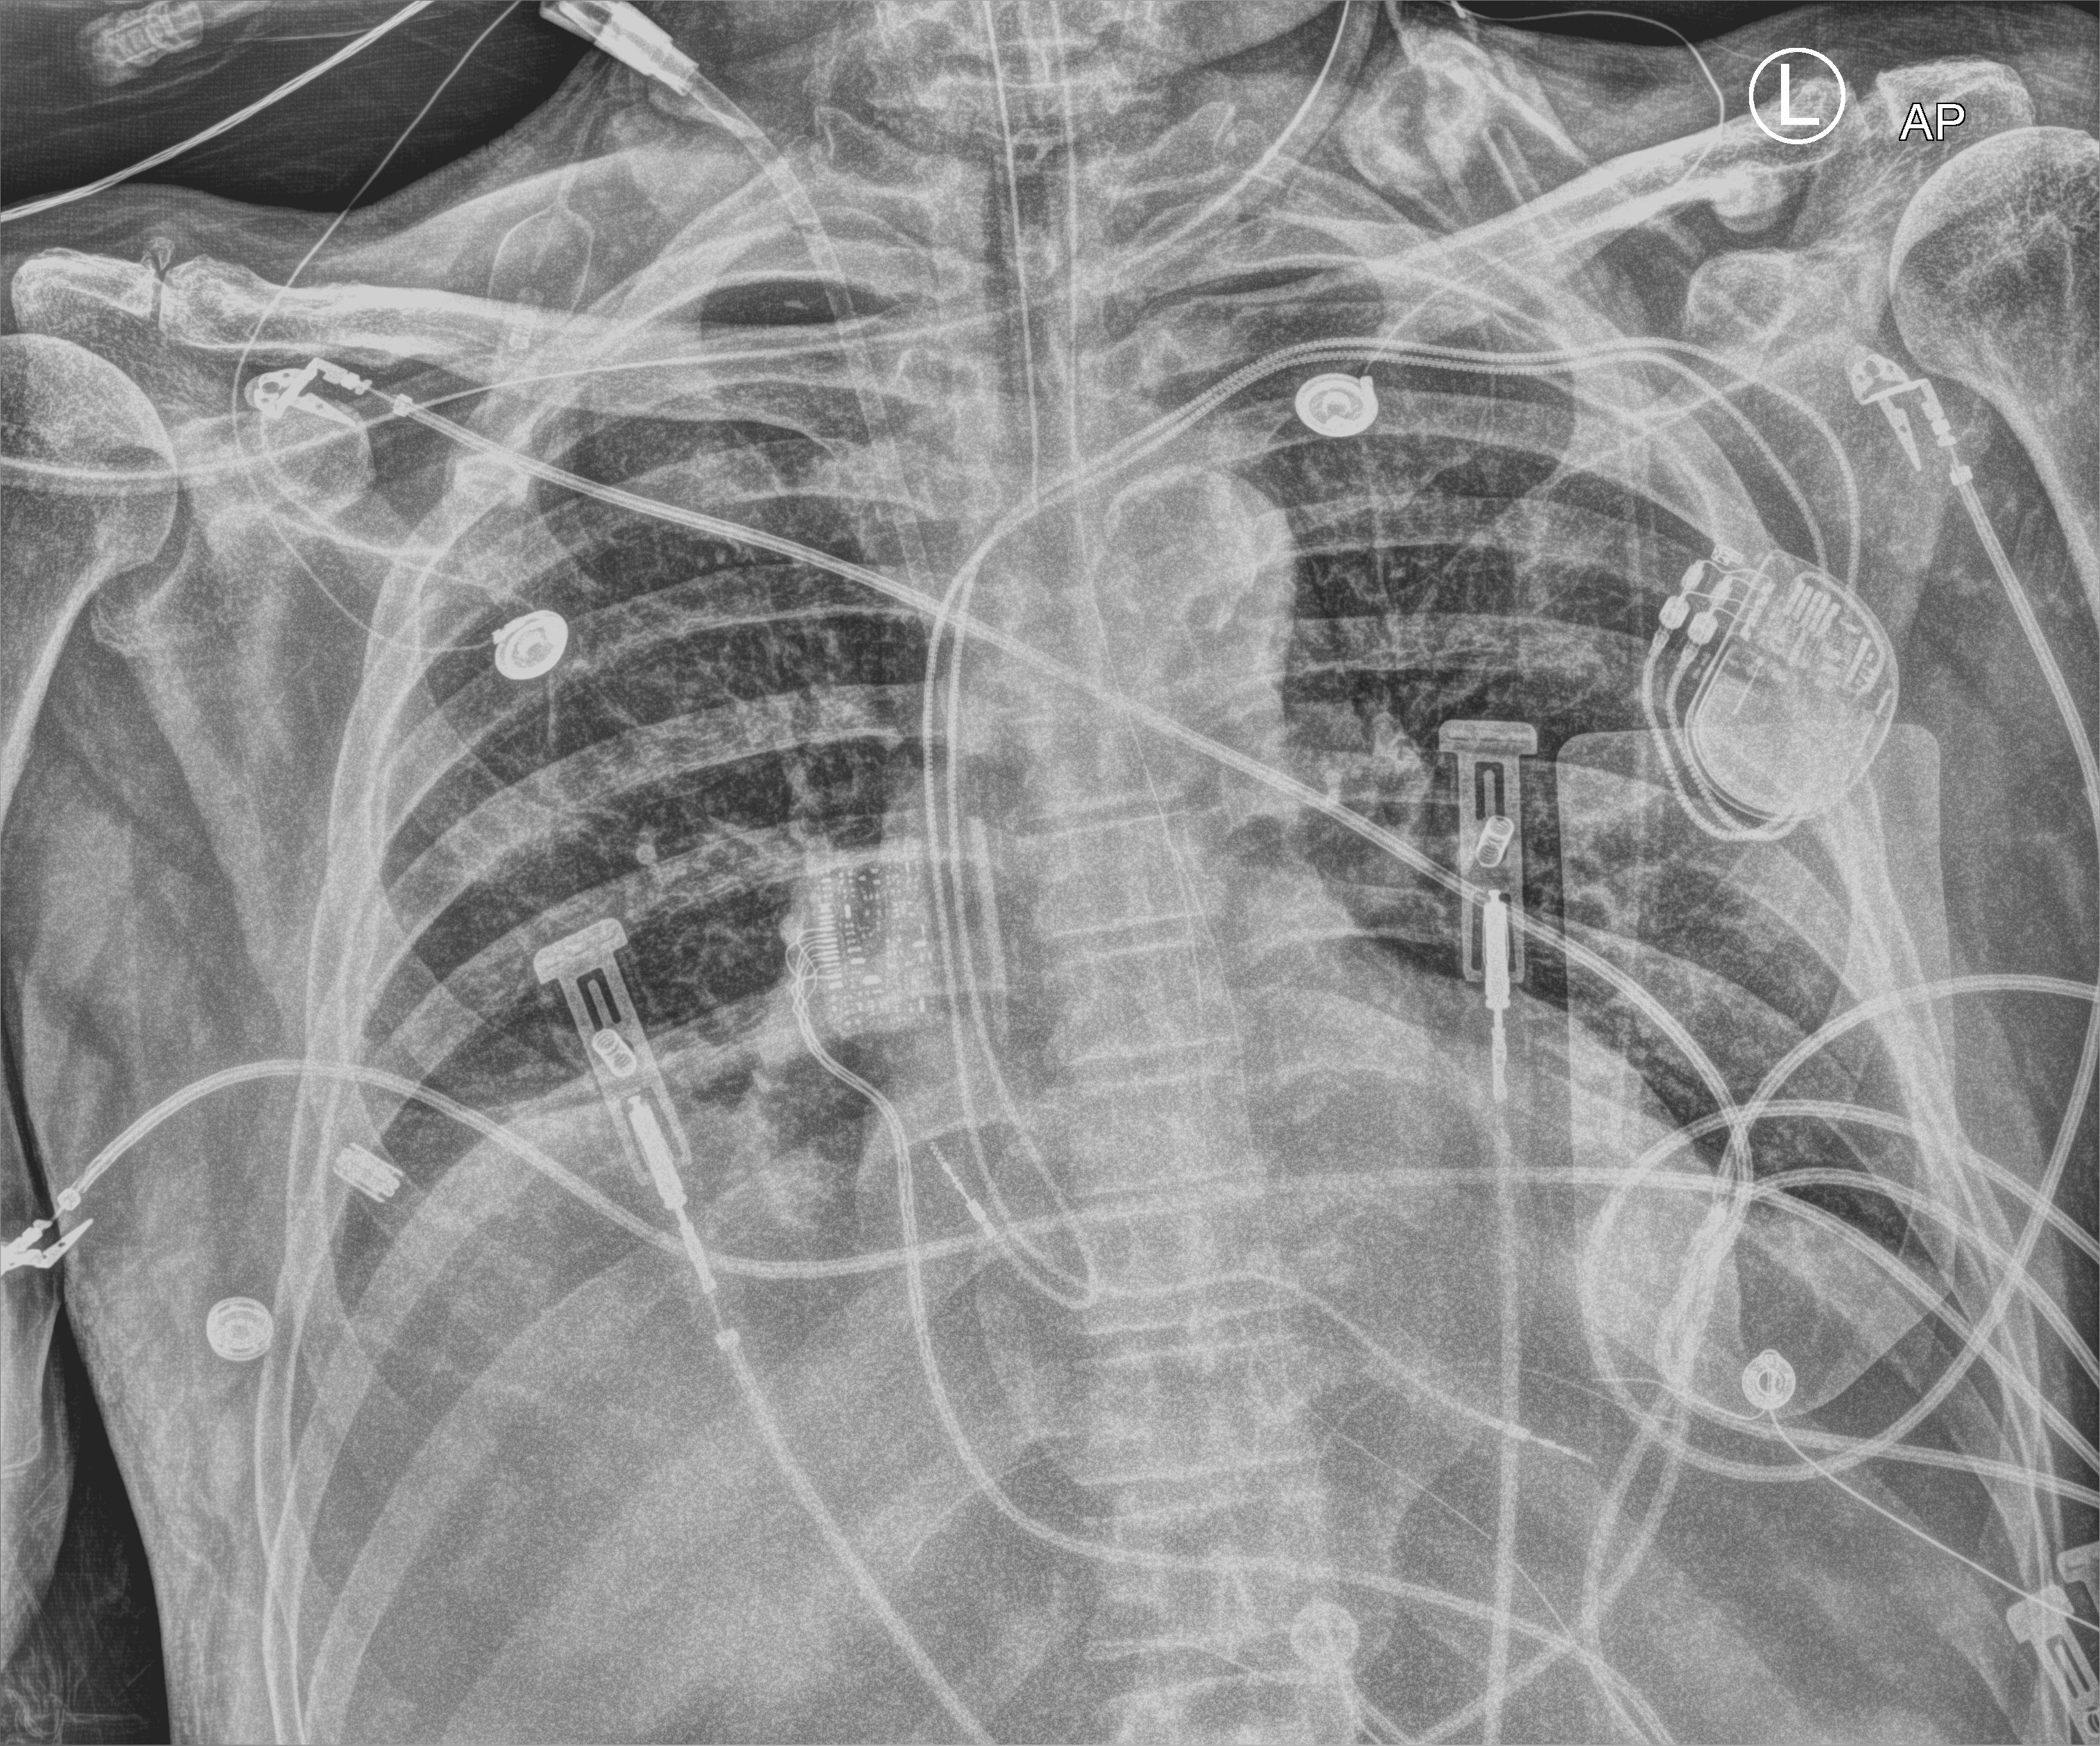
Bedside chest radiograph (computed radiography). Patient hospitalised with COVID-19; male, aged 60–74 years.
Hospital-stay facts (about this admission, not read from this image; timing relative to this image not recorded):
- admitted to intensive care during this hospital stay: yes